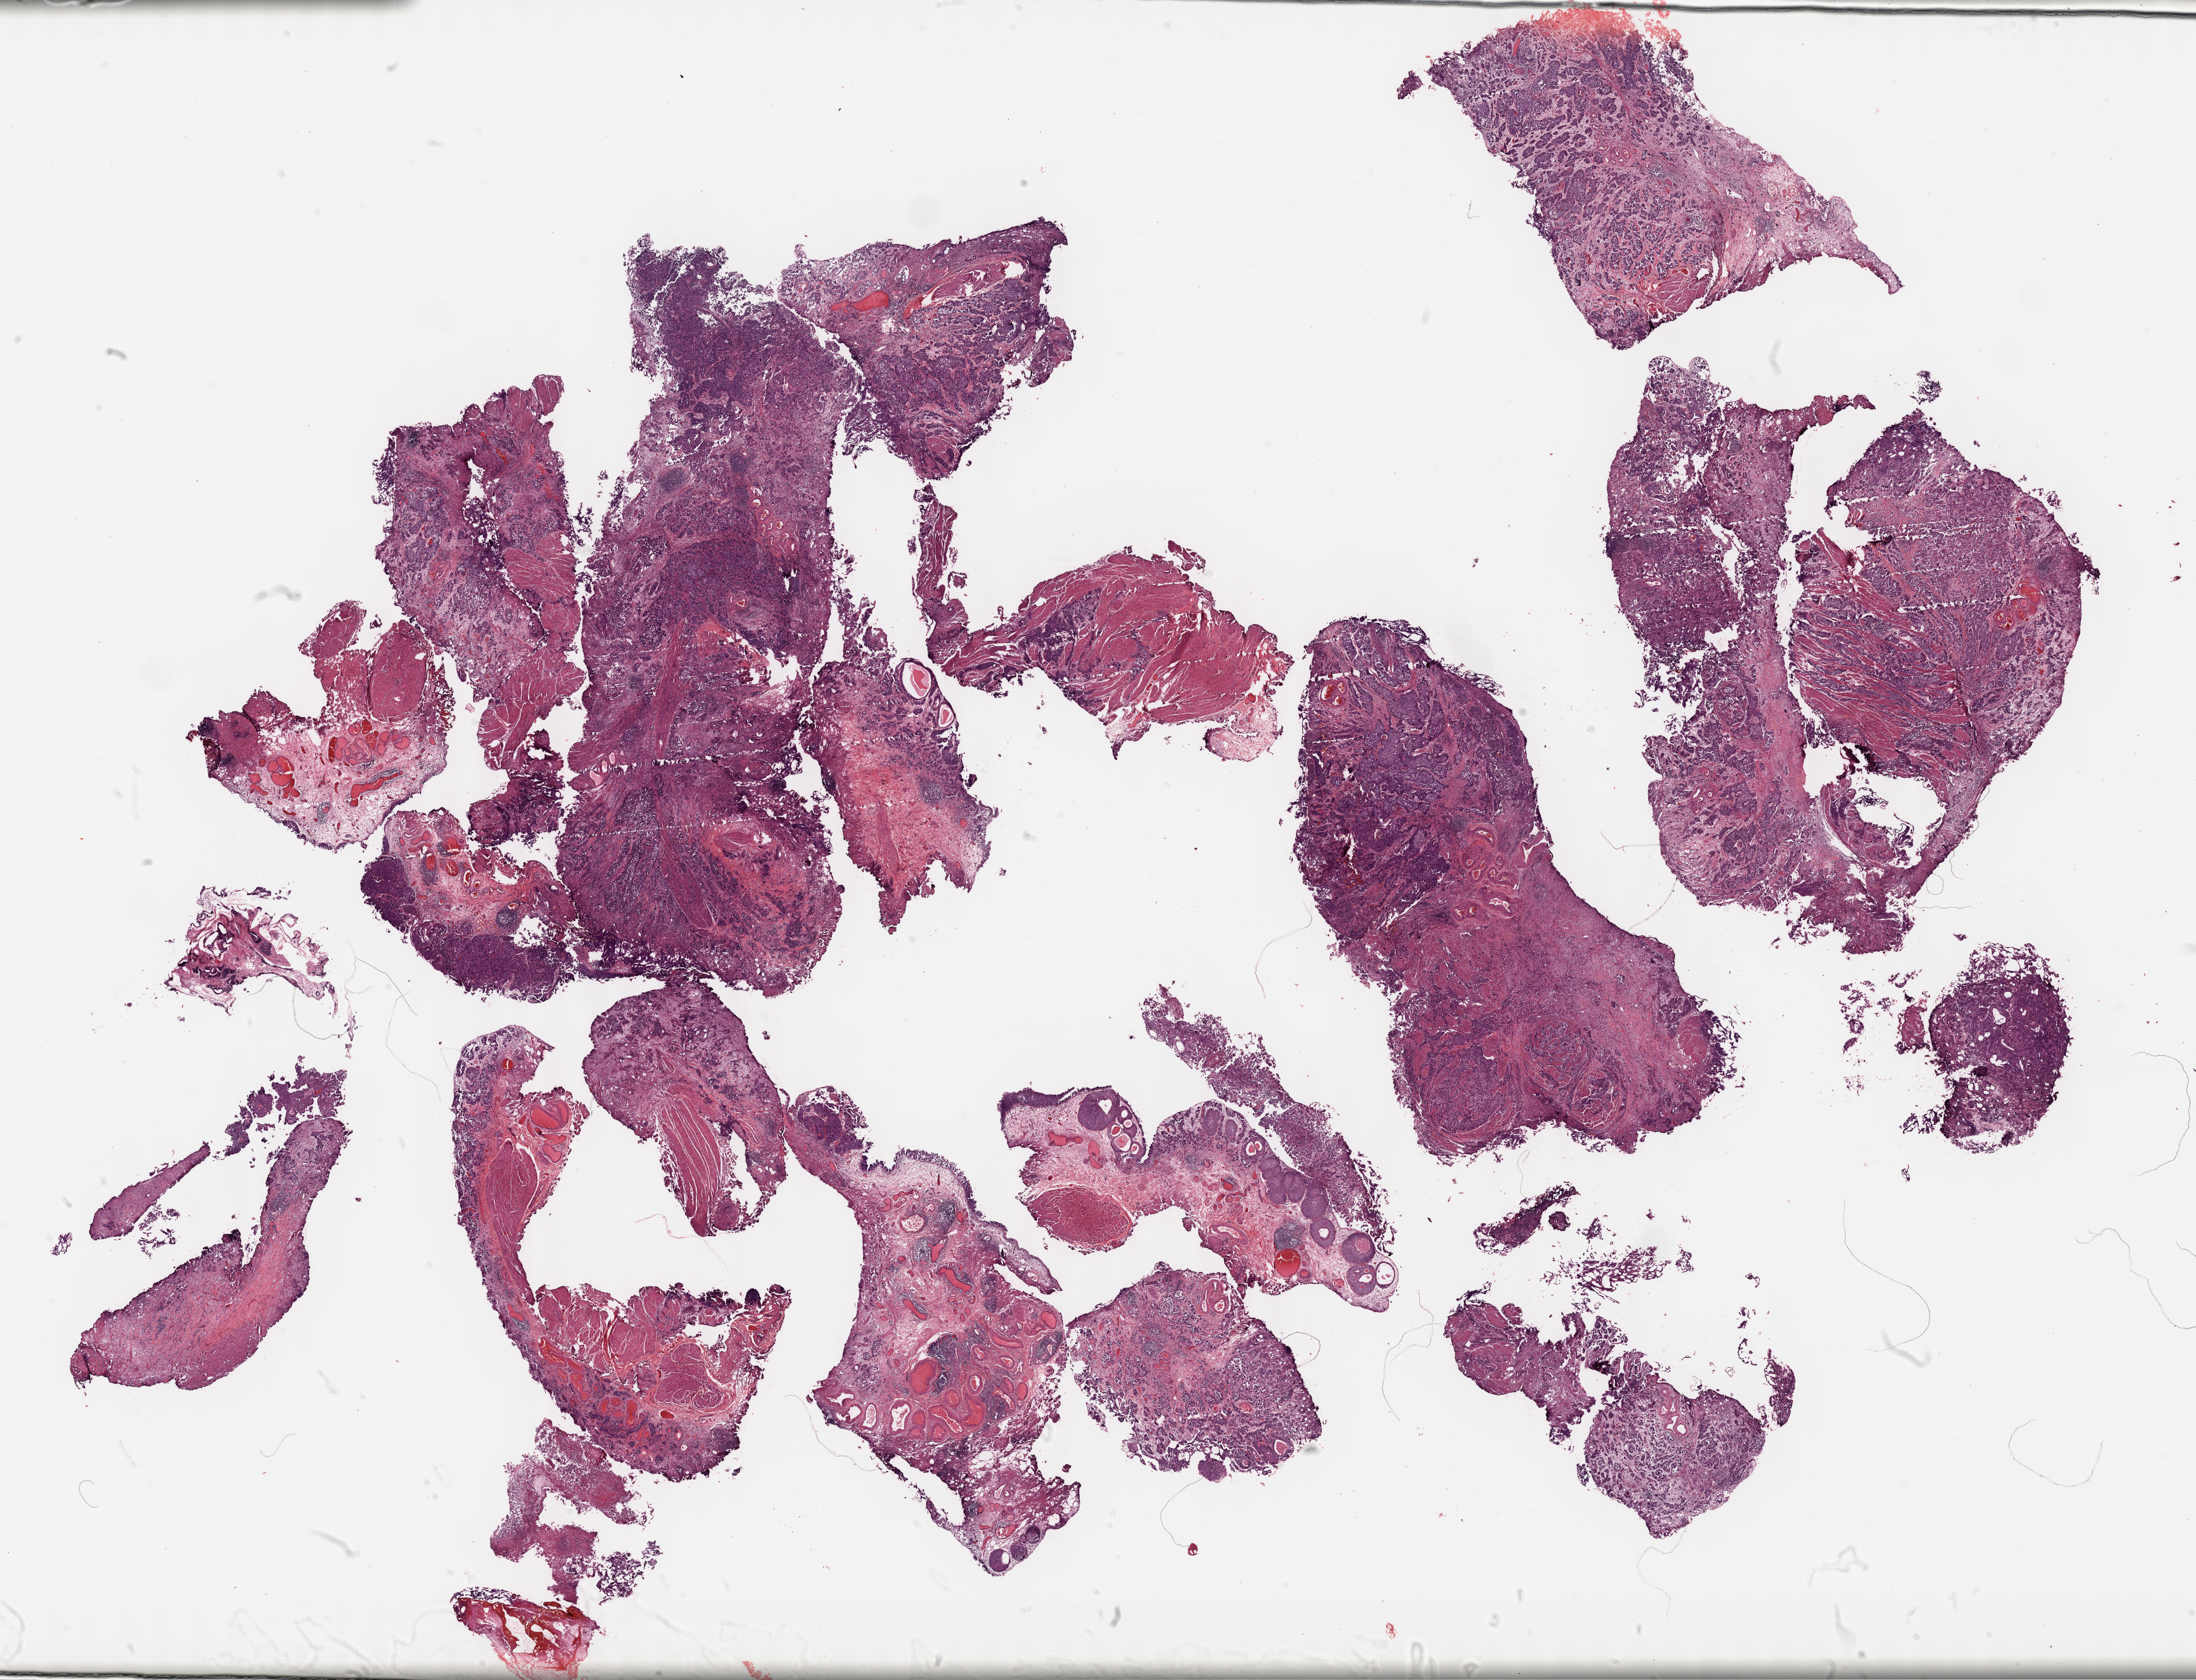
Whole-slide histology image, H&E-stained — shown as a low-resolution overview of the whole scanned area (about 30.7 x 23.5 mm, slide scanned at 40x). FFPE section. Primary tumour sample from the bladder. Male, age 69 years at initial diagnosis. Histologic grade: high grade.
AJCC pathologic stage: IV (5th edition). Pathologic diagnosis: Transitional cell carcinoma.